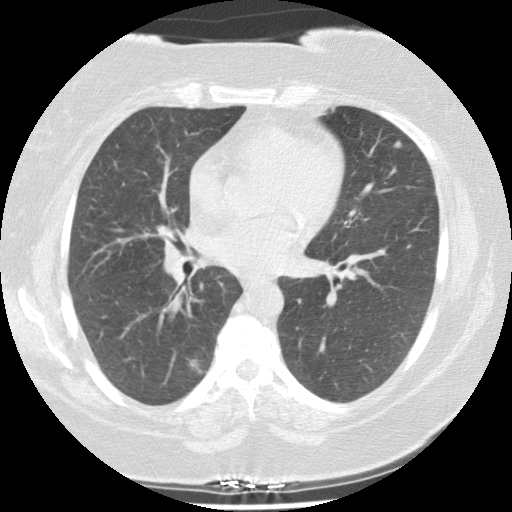
Low-dose screening chest CT, one axial slice; slice 77 of 131 in the series (ordered by position); 140 kVp; lung window (W 1500 / L -600 HU); 2.5 mm slice thickness; 512 × 512 image matrix.
Annotated regions visible in this slice (manually delineated by an expert):
- lesion 1 (tumor, lower lobe of right lung): bounding box <190,360,202,373> (left, top, right, bottom; pixels)